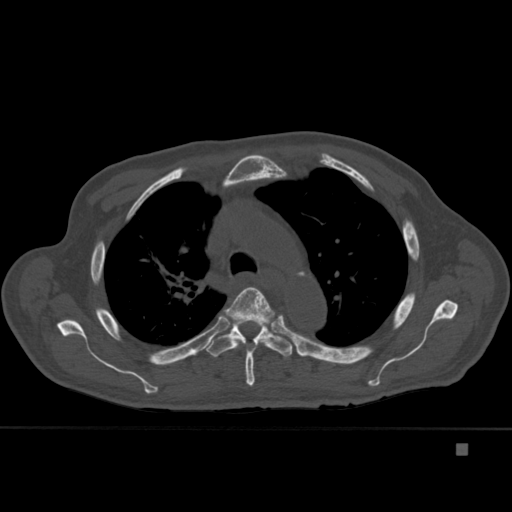
CT including the spine, one axial slice. Slice 314 of 451 in the series (ordered by position). Bone window (W 1800 / L 400 HU). 512 × 512 image matrix, field of view 378 × 378 mm. Male patient, age 75 years. Case-level facts recorded for this patient, not image findings: primary cancer: prostate.
Structures marked on this image (semi-automatically segmented with operator editing):
- T4 vertebra: bounding box [x1, y1, x2, y2] px = [224, 287, 278, 387]
- T5 vertebra: [206, 317, 293, 358]